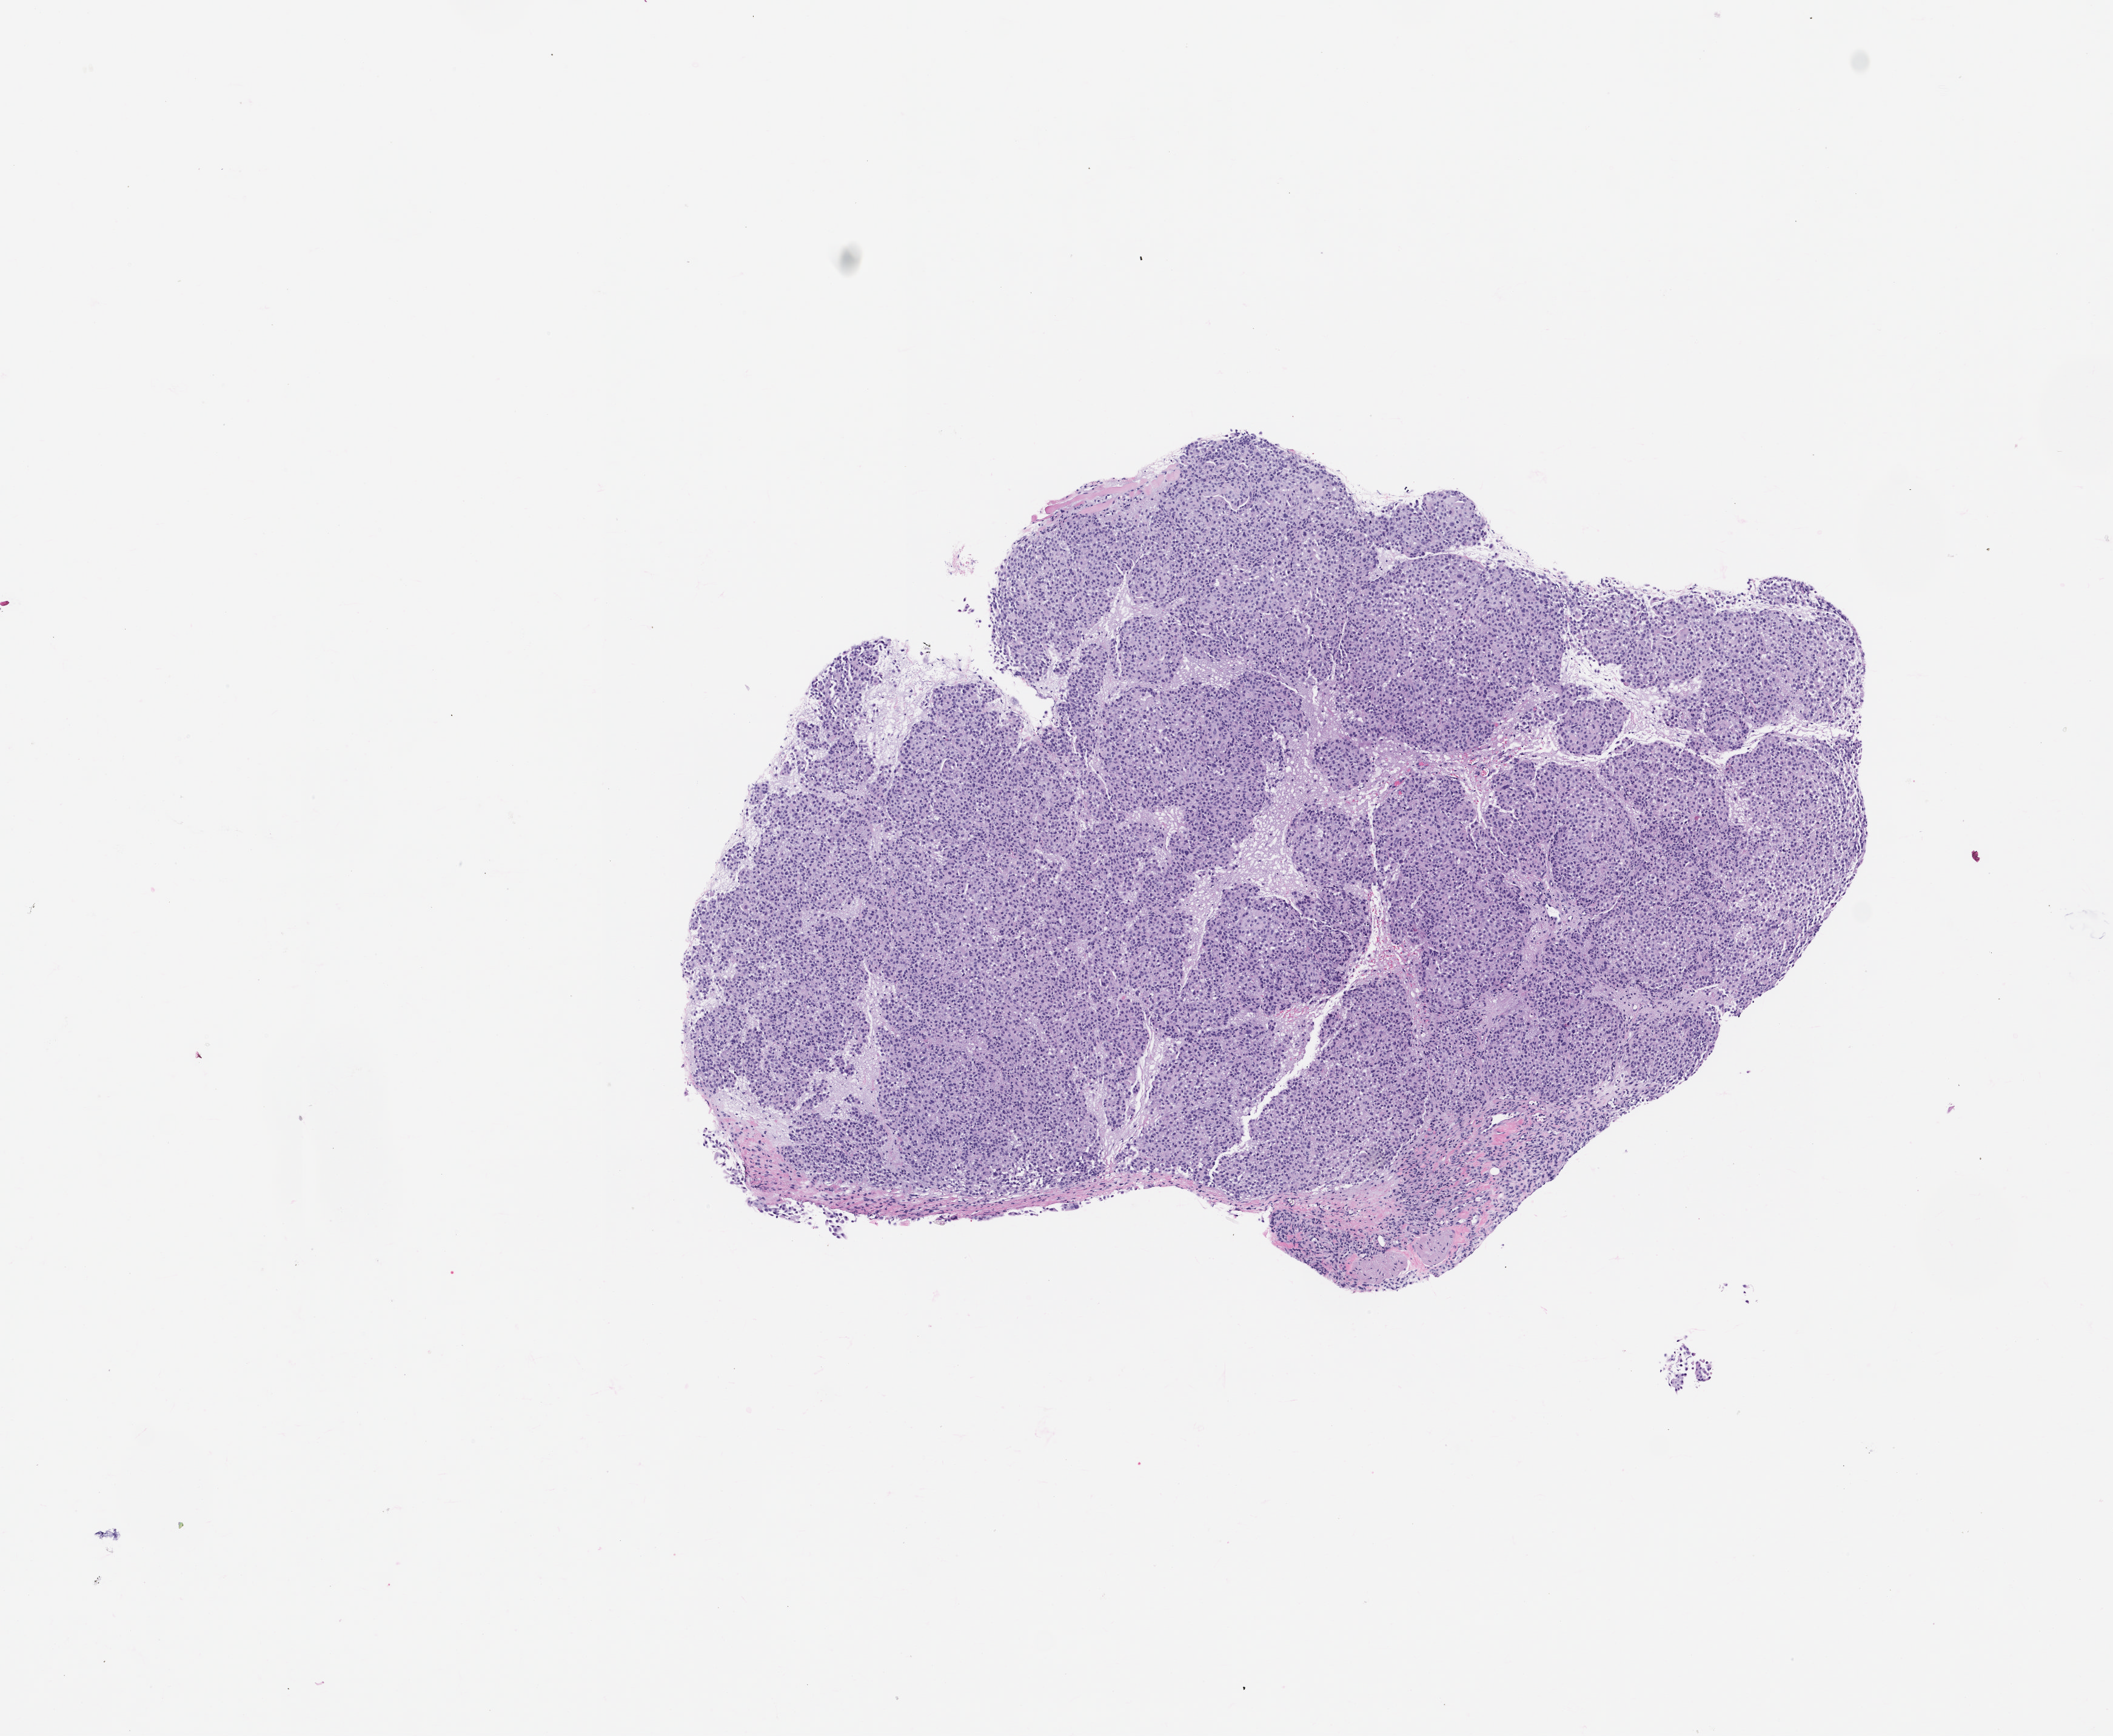
H&E whole-slide image of a patient-derived xenograft (PDX) tumor grown in a mouse, passage 0 — a low-resolution overview of the entire scanned area, about 7.0 x 5.7 mm. Formalin-fixed, paraffin-embedded (FFPE) tissue. Originating tumor site category: bladder.
• originating patient diagnosis: Transitional Cell Carcinoma